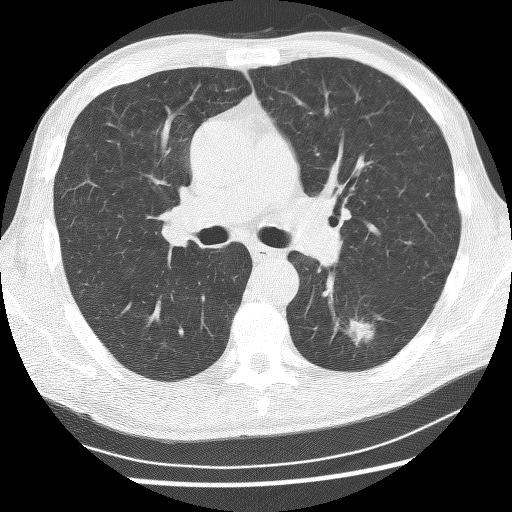
Low-dose screening chest CT, one axial slice; position 151 of 253 along the scan axis; lung window (W 1500 / L -600 HU); 512 × 512 image matrix, field of view 340 × 340 mm.
Structures marked on this image (expert manual segmentation):
- lesion 1 (tumor, lower lobe of left lung): bounding box <347,319,374,345> (left, top, right, bottom; pixels)